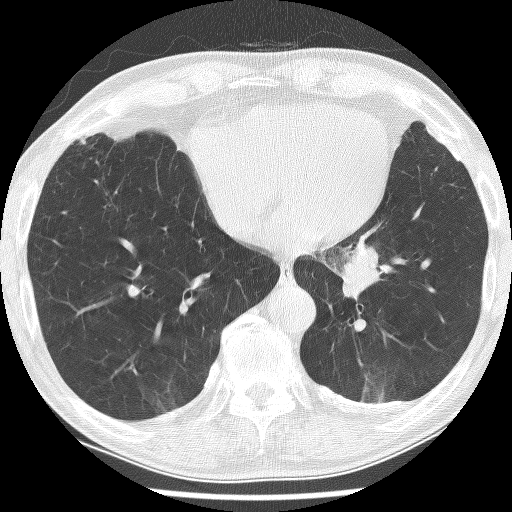
Low-dose screening chest CT, one axial slice; slice 57 of 226 in the series (ordered by position); 120 kVp; lung window (W 1500 / L -600 HU); 512 × 512 image matrix, field of view 320 × 320 mm.
Annotated regions visible in this slice (expert manual segmentation):
- lesion 1 (tumor, lower lobe of left lung): bounding box (x1, y1, x2, y2) in pixels: (343, 246, 381, 301)